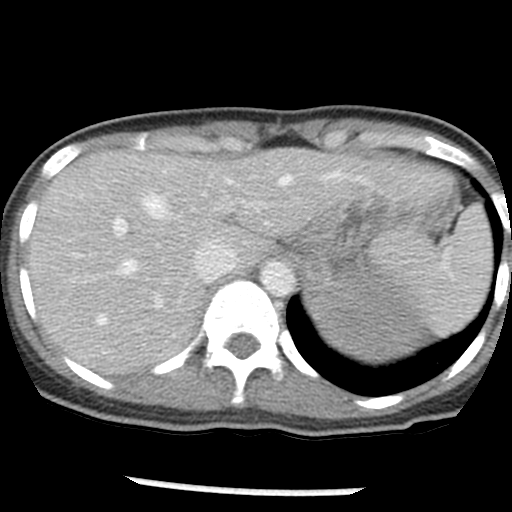
Contrast-enhanced abdominal CT, one axial slice; position 39 of 54 along the scan axis; 120 kVp; intravenous contrast given; soft-tissue window (W 400 / L 40 HU); 512 × 512 image matrix, field of view 240 × 240 mm. Patient: female, 33 years. From the clinical record (not read from this slice): diagnosis: adrenocortical carcinoma; tumour side: left adrenal; tumour size at pathology: 11 cm; Ki-67 index: 20 %; stage (as recorded): 2.
Structures marked on this image (semi-automatic segmentation, software-assisted and operator-edited):
- mass: bounding box [x1, y1, x2, y2] px = [305, 270, 424, 362]